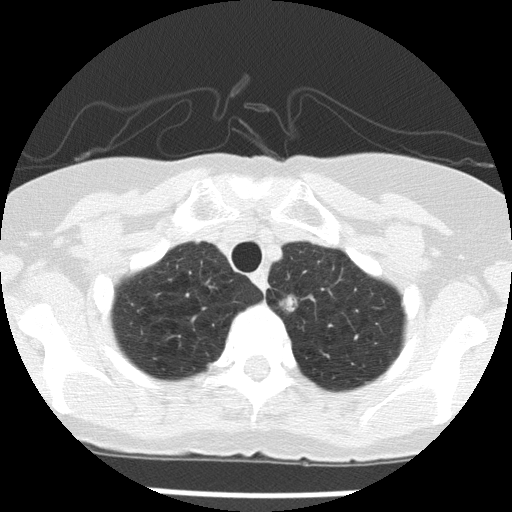
Low-dose screening chest CT, one axial slice; position 124 of 143 along the scan axis; 120 kVp; lung window (W 1500 / L -600 HU); 2 mm slice thickness; 512 × 512 image matrix, field of view 276 × 276 mm.
Outlined on this slice (manually delineated by an expert):
- lesion 1 (tumor, upper lobe of left lung): box from (x=280, y=295) to (x=297, y=312) px